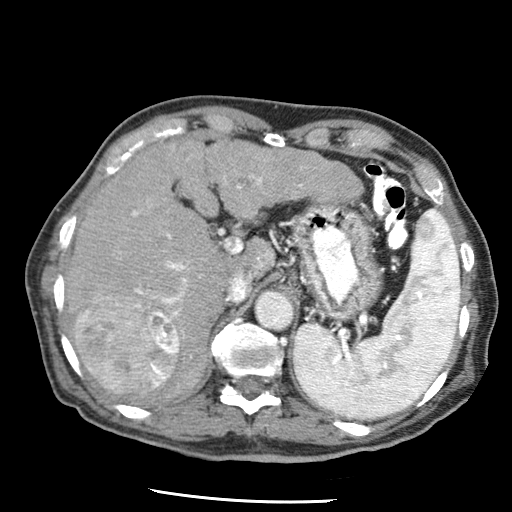
Contrast-enhanced abdominal CT (liver protocol), one axial slice; slice 38 of 79 in the series (ordered by position); soft-tissue window (W 400 / L 40 HU); 2.5 mm slice thickness; 512 × 512 image matrix, field of view 320 × 320 mm. Case-level facts recorded for this patient, not image findings: diagnosis: hepatocellular carcinoma (patient treated with transarterial chemoembolisation; whether this scan precedes or follows treatment is not stated here); TNM stage (as recorded): Stage-IIIA; Child-Pugh class: A; tumour differentiation: moderately differentiated; tumour size: 7 cm.
Annotated regions visible in this slice (semi-automatically segmented with operator editing):
- liver parenchyma outside the tumour (the mass and vessels are separate outlines, so this box may not span the whole liver): bounding box (x1, y1, x2, y2) in pixels: (64, 140, 362, 401)
- mass: (75, 295, 179, 396)
- liver vessels: (119, 175, 302, 320)